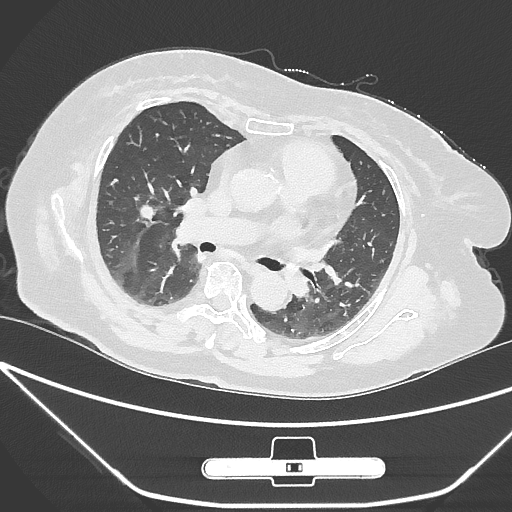
Chest CT, one axial slice. Position 153 of 245 along the scan axis. 120 kVp. Lung window (W 1500 / L -600 HU). 1 mm slice thickness. 512 × 512 image matrix, field of view 365 × 365 mm. Female patient, age 65 years. Case-level facts recorded for this patient, not image findings: clinical TNM (as recorded): T1c N0 M0; histopathological grade: G3.
Outlined on this slice (rectangle marked by the reading radiologist):
- lung tumour (recorded histology: adenocarcinoma): bounding box [x1, y1, x2, y2] px = [134, 195, 154, 224]